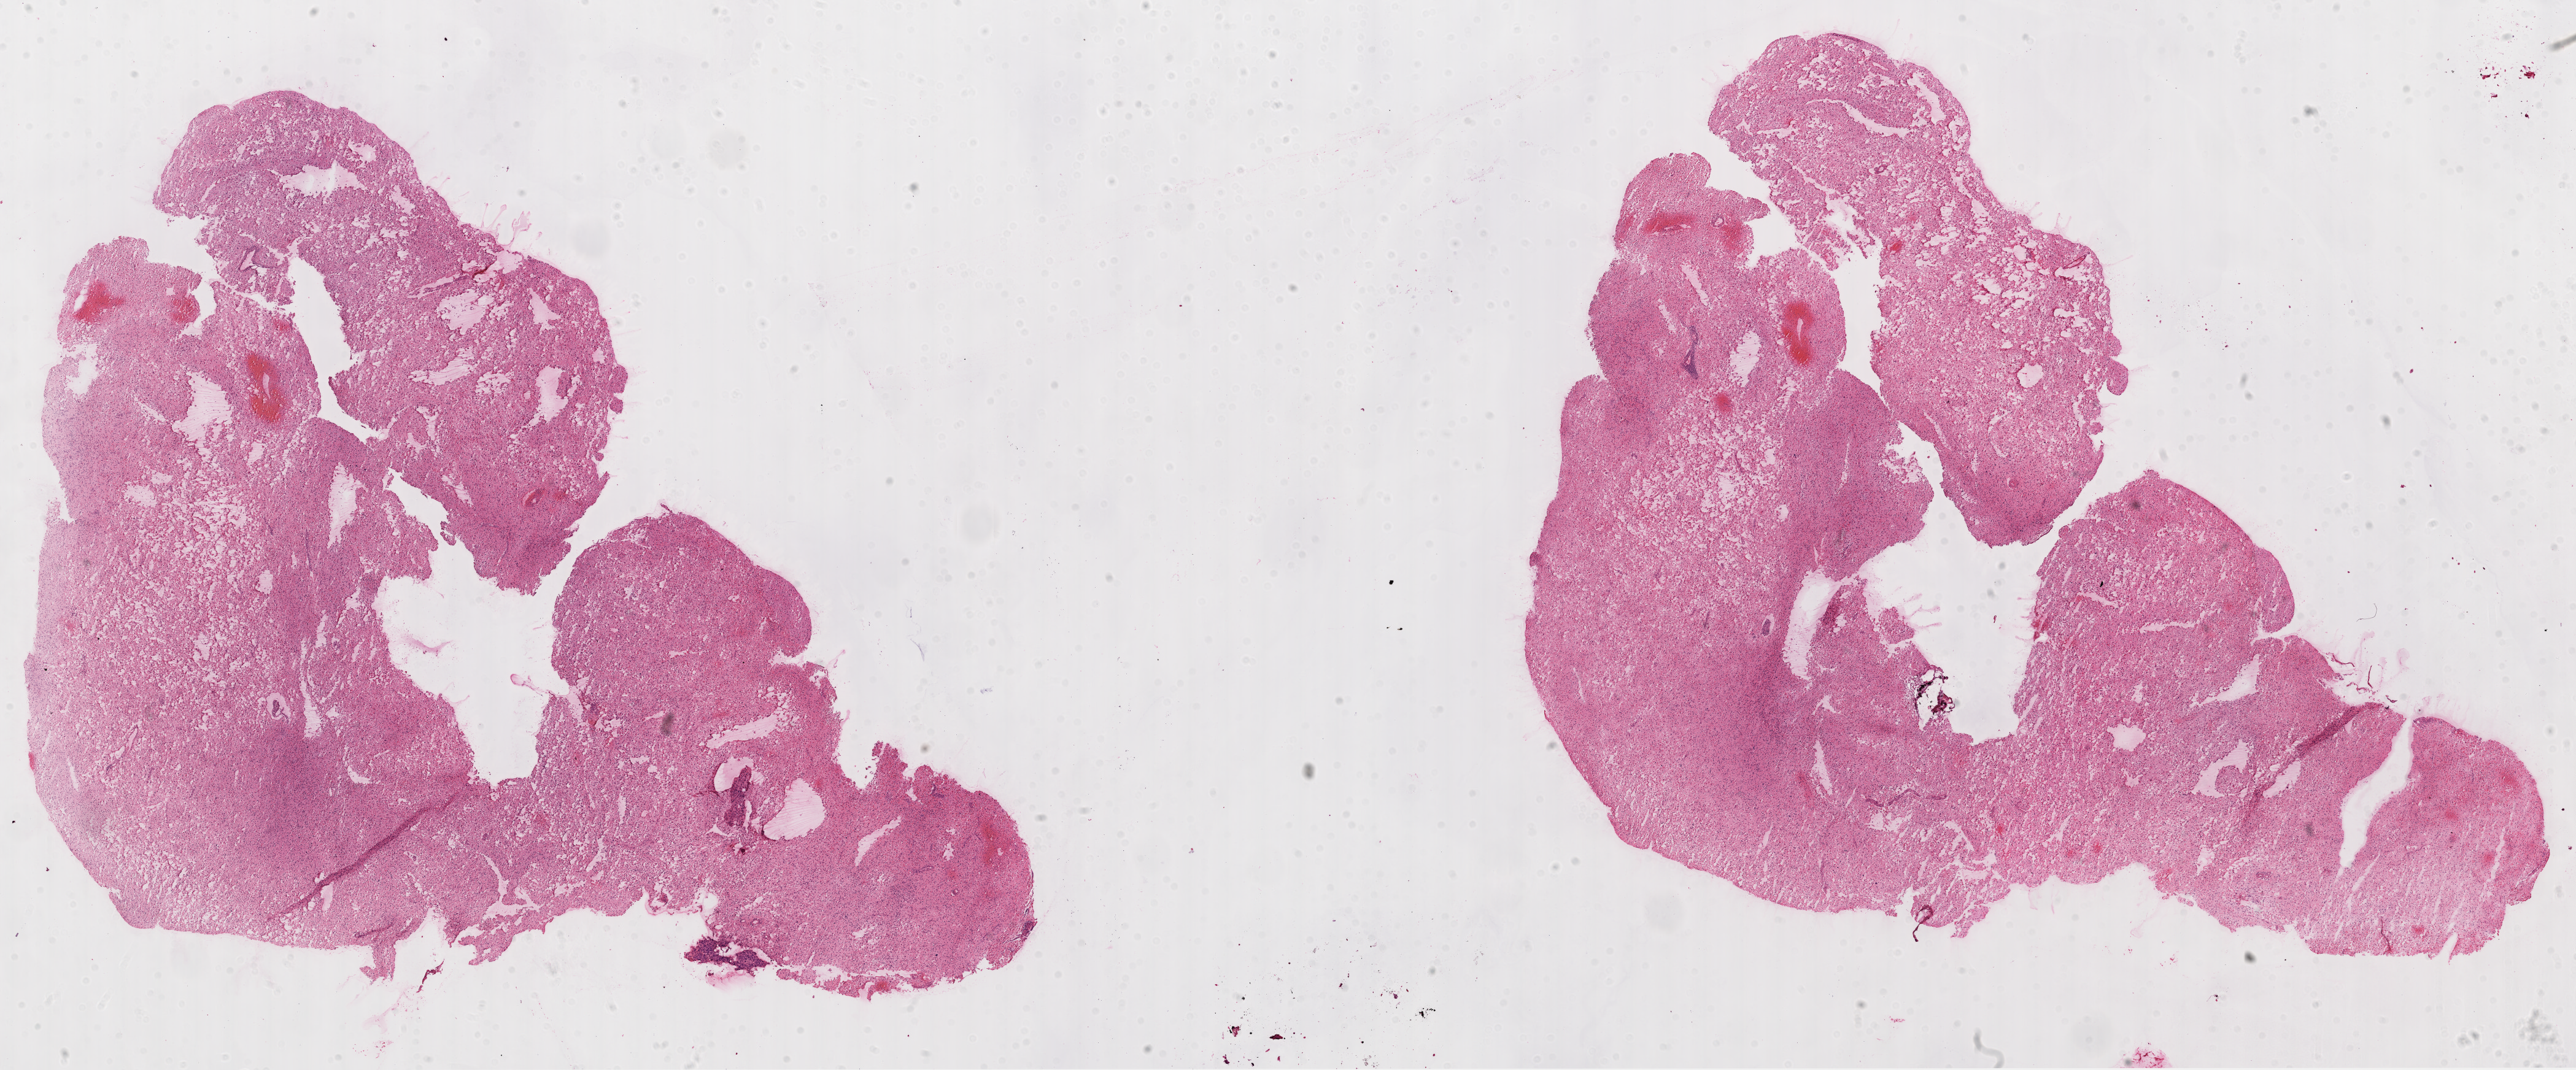
Digitized H&E-stained tissue section (whole slide), whole scanned area (about 33.8 x 14.1 mm) shown as a low-resolution overview. Frozen section from the top of the tissue portion. Sample: primary tumour, brain. Patient: female, age at initial diagnosis 36 years. Pathologist review of this section (percent, as recorded): tumour cells 95%, tumour nuclei 100%, normal cells 0%, stromal cells 0%, necrosis 5%.
- pathologic diagnosis: Glioblastoma